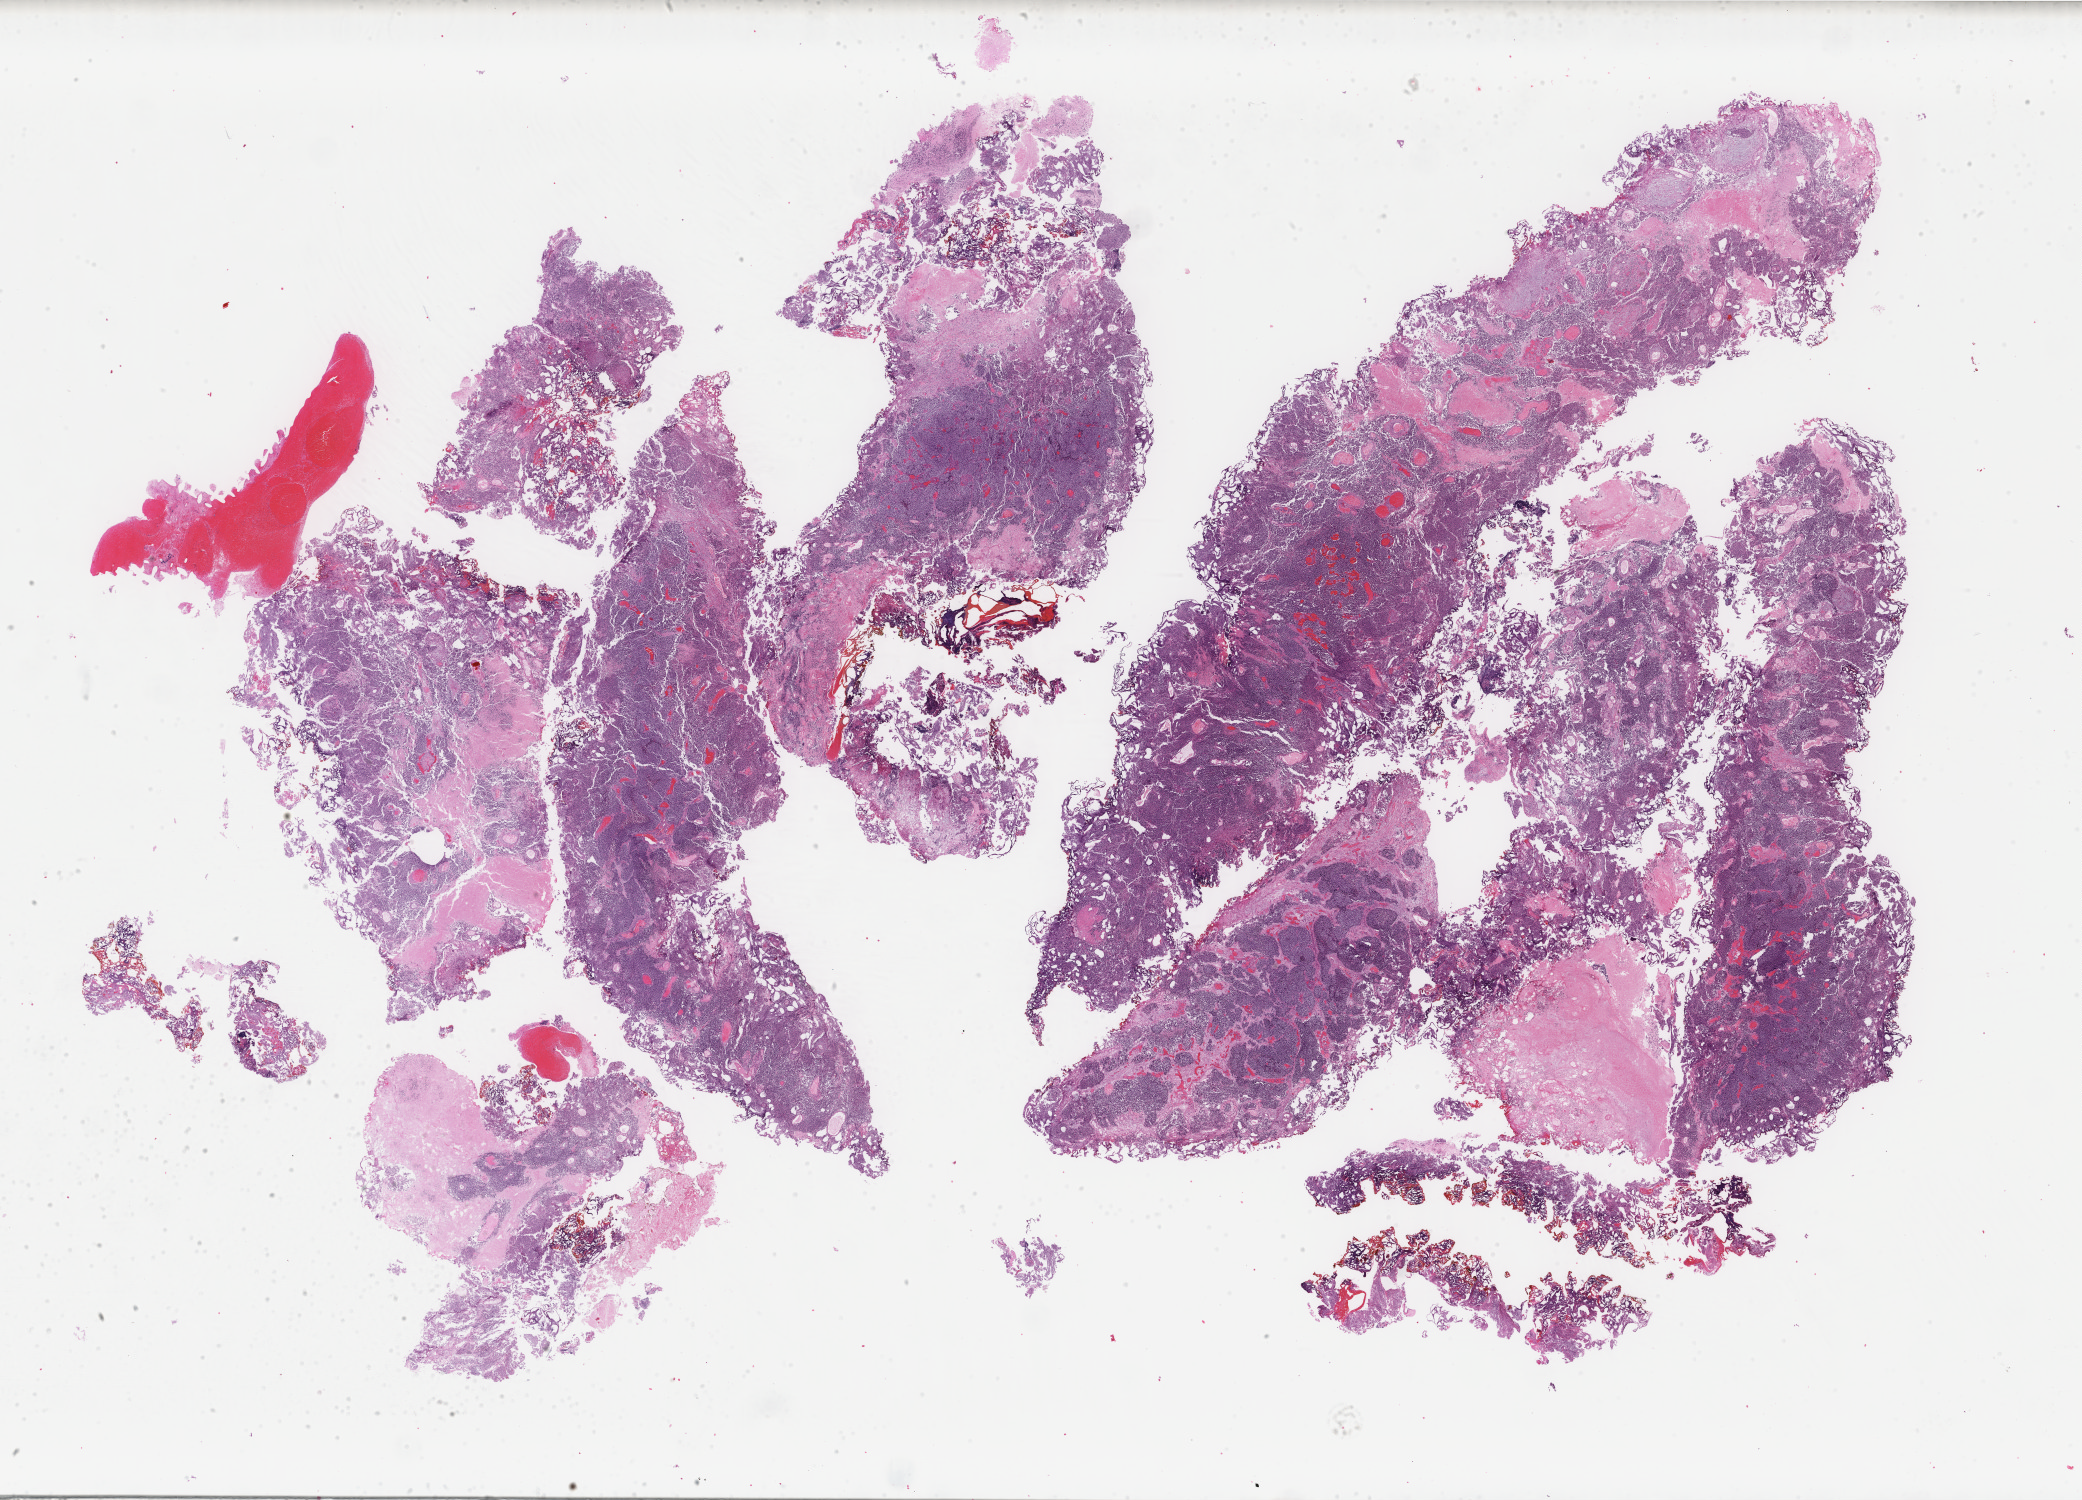
H&E whole-slide image — a low-resolution overview of the entire scanned area, about 33.1 x 23.8 mm (from a 40x scan), formalin-fixed paraffin-embedded (FFPE) diagnostic section, bladder, primary tumour sample. Patient: male, age at initial diagnosis 77 years. Histologic grade: high grade.
Histologic diagnosis: Transitional cell carcinoma. AJCC pathologic stage: II (6th edition).